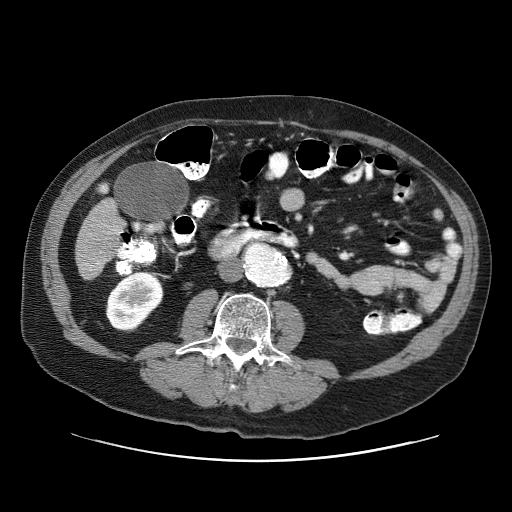
Contrast-enhanced abdominal CT (liver protocol), one axial slice. Position 6 of 87 along the scan axis. Reconstruction kernel STANDARD. 120 kVp. One of 3 acquisitions stored at this slice position. Soft-tissue window (W 400 / L 40 HU). 2.5 mm slice thickness. 512 × 512 image matrix, field of view 400 × 400 mm. Case-level facts recorded for this patient, not image findings: diagnosis: hepatocellular carcinoma (patient treated with transarterial chemoembolisation; whether this scan precedes or follows treatment is not stated here); TNM stage (as recorded): Stage-IIIA; Child-Pugh class: A.
Structures marked on this image (semi-automatically segmented with operator editing):
- liver parenchyma outside the tumour (the mass and vessels are separate outlines, so this box may not span the whole liver): bounding box (x1, y1, x2, y2) in pixels: (76, 187, 124, 280)